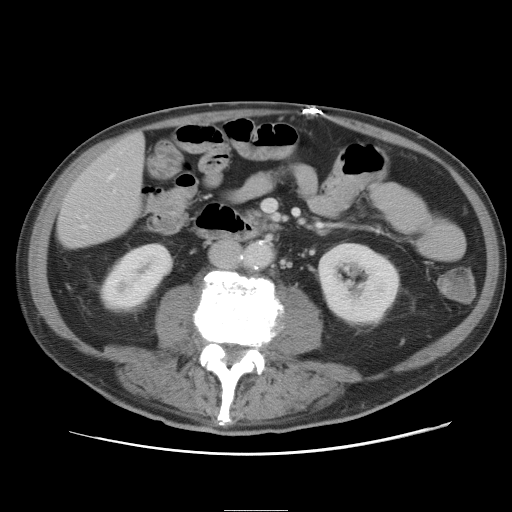
Contrast-enhanced abdominal CT, one axial slice. 120 kVp. Intravenous contrast given. Soft-tissue window (W 400 / L 40 HU). 5 mm slice thickness. 512 × 512 image matrix. Male patient, age 69 years. From the clinical record (not read from this slice): diagnosis: colorectal cancer liver metastases, imaged before liver resection; multiple liver metastases: no; largest metastasis: 8.5 cm; disease in both lobes: no.
Annotated regions visible in this slice (expert manual segmentation):
- hepatic veins: bounding box <84,175,114,227> (left, top, right, bottom; pixels)
- liver: <59,134,144,248>
- planned liver remnant (the part of the liver to remain after resection): <59,134,145,248>